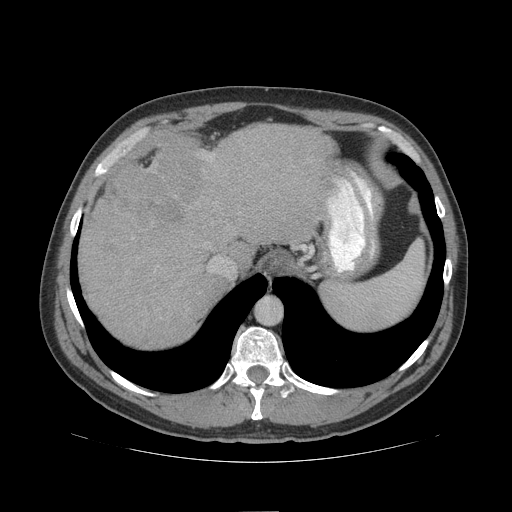
Contrast-enhanced abdominal CT (liver protocol), one axial slice. Slice 82 of 109 in the series (ordered by position). Reconstruction kernel STANDARD. 140 kVp. Soft-tissue window (W 400 / L 40 HU). 2.5 mm slice thickness. 512 × 512 image matrix, field of view 420 × 420 mm. Case-level facts recorded for this patient, not image findings: diagnosis: hepatocellular carcinoma (patient treated with transarterial chemoembolisation; whether this scan precedes or follows treatment is not stated here); TNM stage (as recorded): Stage-IIIB; Child-Pugh class: A; tumour differentiation: poorly differentiated; tumour nodularity: multinodular.
Structures marked on this image (semi-automatic segmentation, software-assisted and operator-edited):
- abdominal aorta: box from (x=257, y=298) to (x=281, y=325) px
- liver parenchyma outside the tumour (the mass and vessels are separate outlines, so this box may not span the whole liver): (x=78, y=124)–(x=350, y=346)
- mass: (x=113, y=134)–(x=218, y=233)
- liver vessels: (x=337, y=180)–(x=352, y=194)